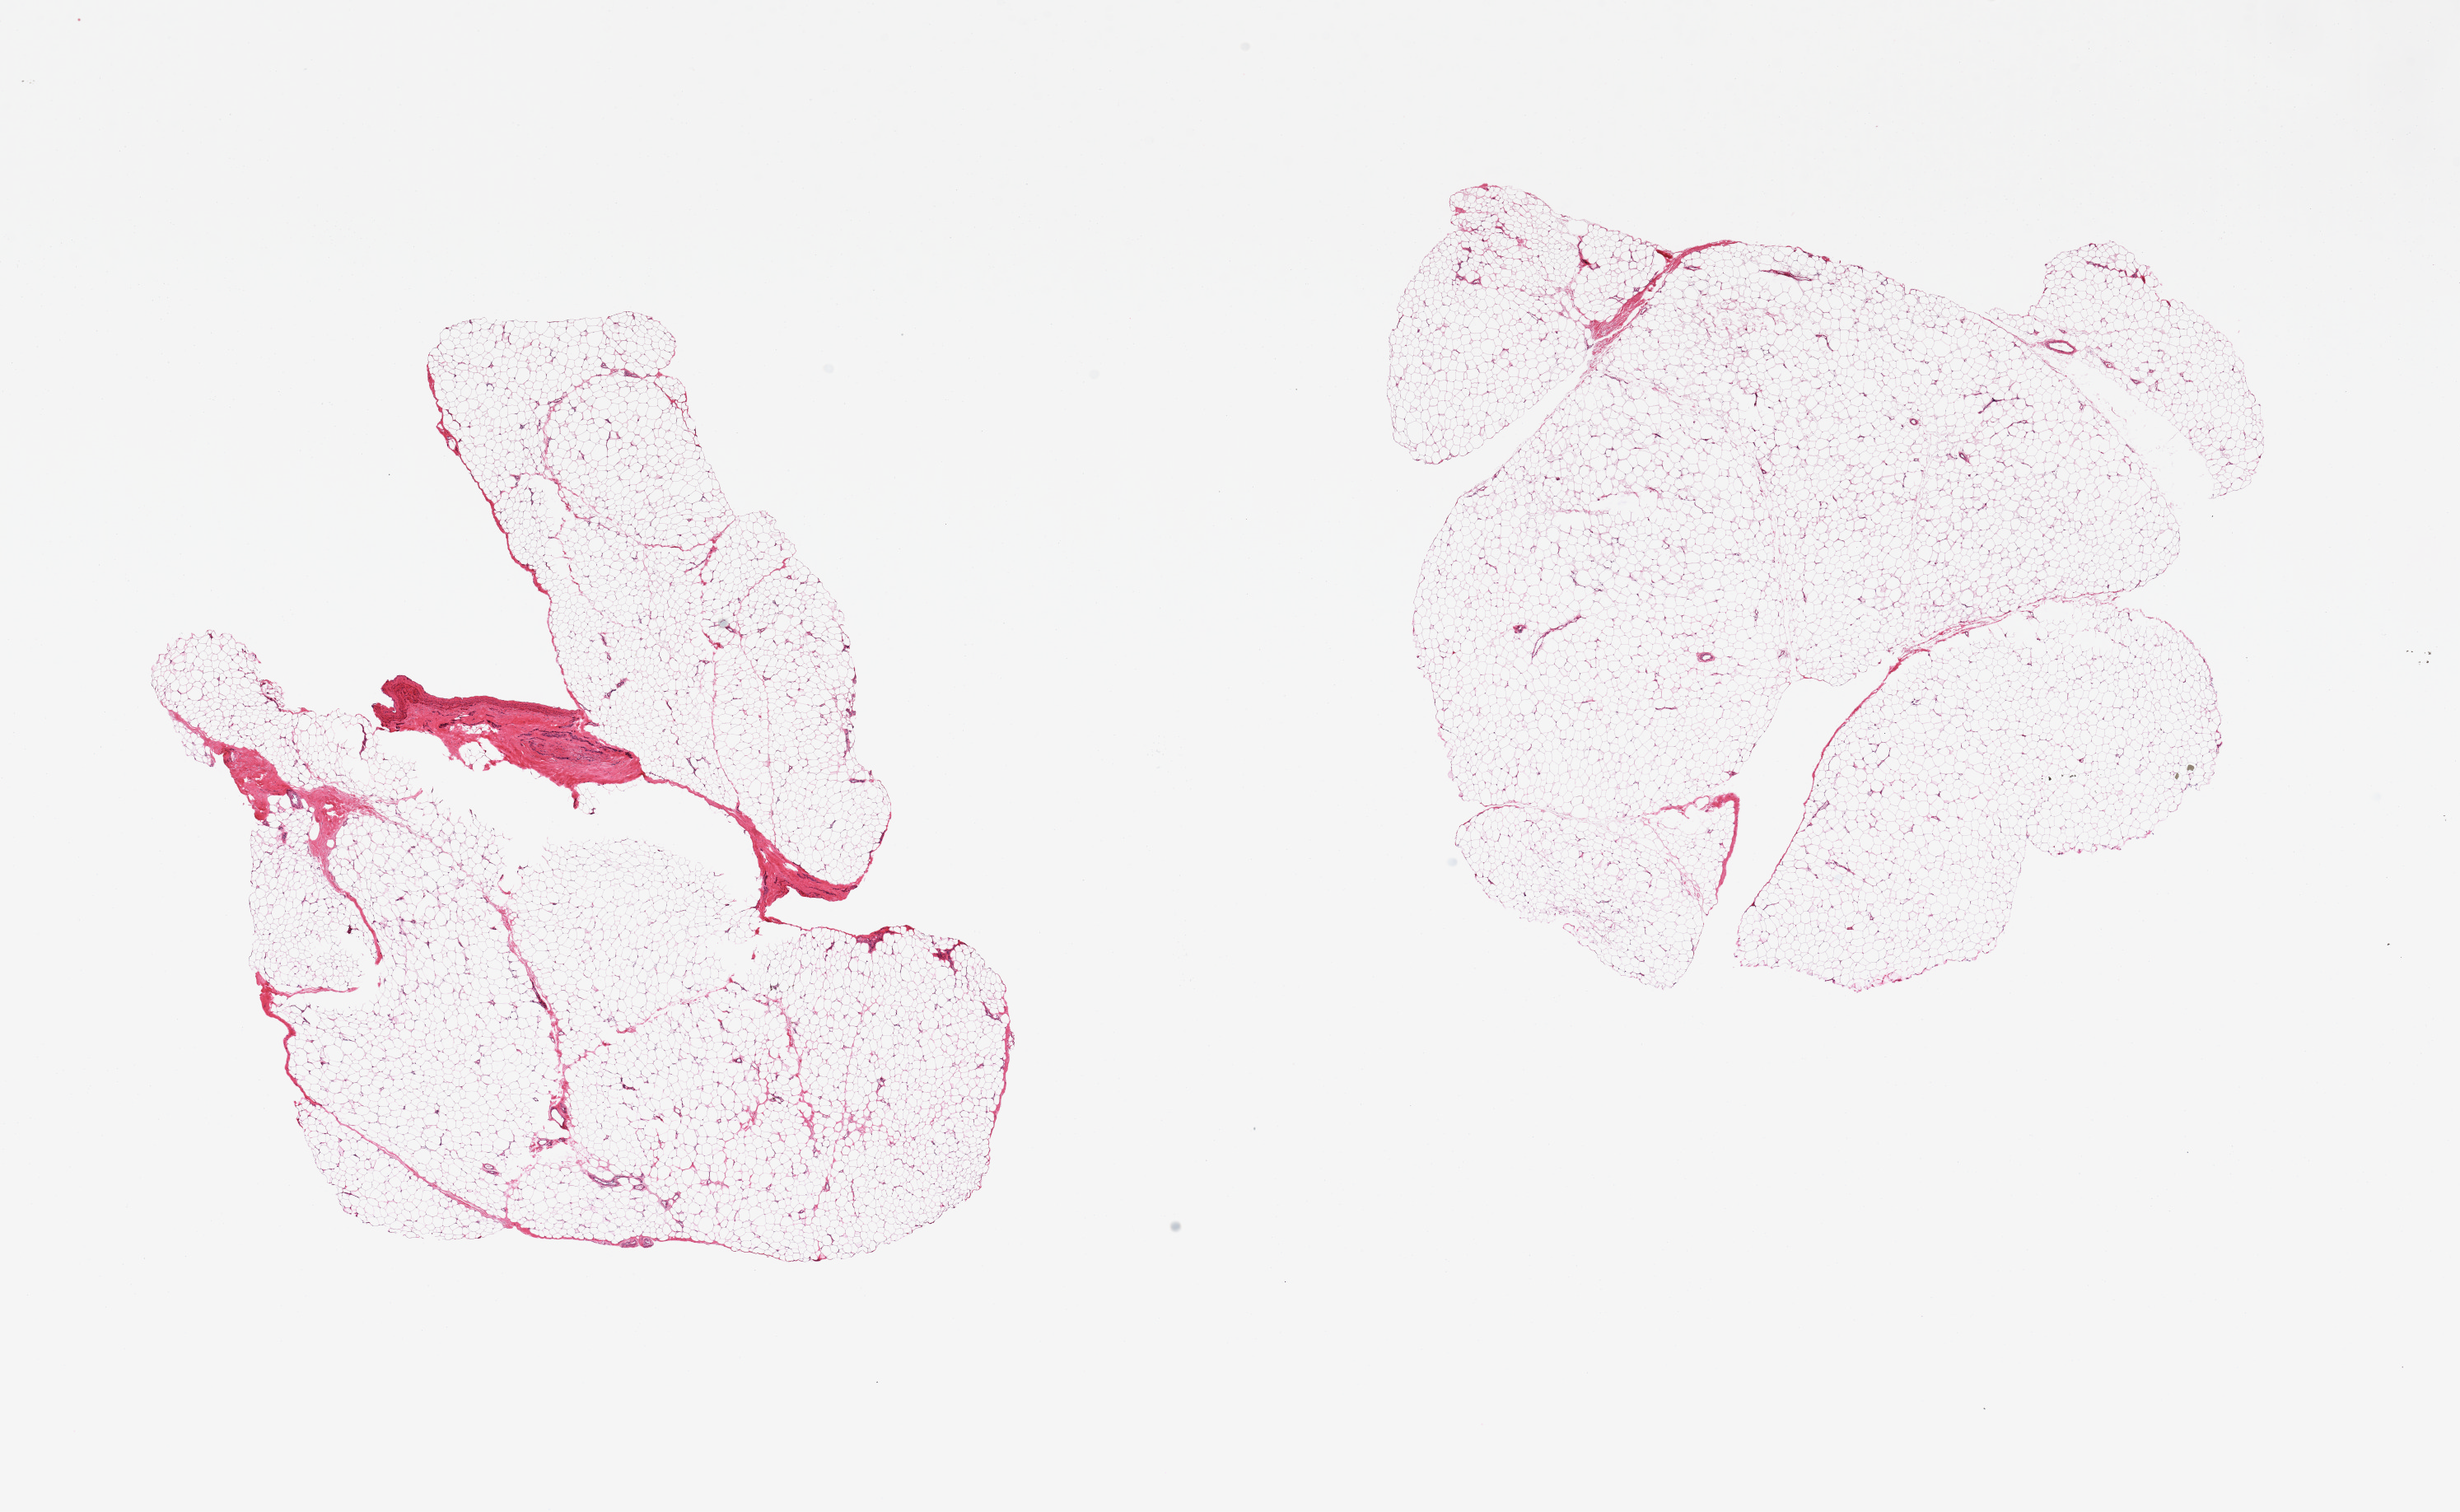
Whole-slide image, hematoxylin and eosin (H&E) stain, whole scanned area (about 23.6 x 14.5 mm, acquisition: 20x scan) shown as a low-resolution overview. PAXgene-fixed, paraffin-embedded tissue. Section of adipose tissue (target tissue). Tissue donor sample.
* review note (as recorded): 2 pieces, fascial elements are ~5-10% of tissue